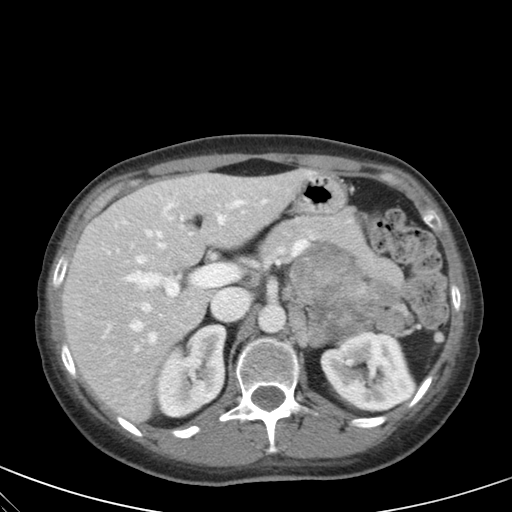
Contrast-enhanced abdominal CT, one axial slice; intravenous contrast given; soft-tissue window (W 400 / L 40 HU); 512 × 512 image matrix, field of view 350 × 350 mm. Patient: female, 28 years. Case-level facts recorded for this patient, not image findings: diagnosis: adrenocortical carcinoma; tumour side: left adrenal; tumour size at pathology: 7 cm; Ki-67 index: 40 %; stage (as recorded): 4.
Annotated regions visible in this slice (semi-automatic segmentation, software-assisted and operator-edited):
- mass: box from (x=292, y=243) to (x=404, y=346) px